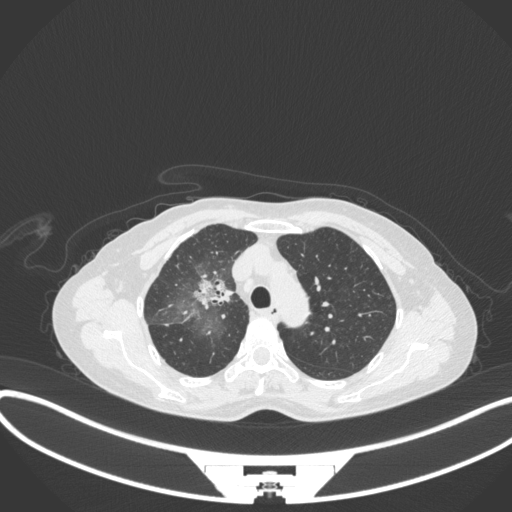
Chest CT, one axial slice. Position 234 of 311 along the scan axis. Lung window (W 1500 / L -600 HU). 1 mm slice thickness. 512 × 512 image matrix, field of view 400 × 400 mm. Female patient, age 59 years. Case-level facts recorded for this patient, not image findings: clinical TNM (as recorded): T3 N0 M0; histopathological grade: G1.
Structures marked on this image (rectangle marked by the reading radiologist):
- lung tumour (recorded histology: adenocarcinoma): box from (x=184, y=267) to (x=237, y=314) px